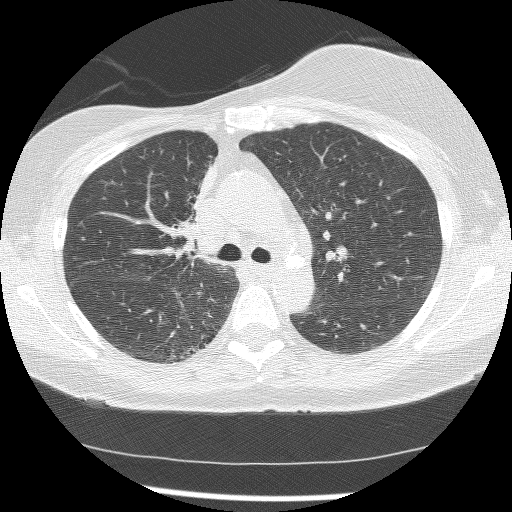
Chest CT (low-dose screening protocol), one axial image, baseline annual screen, lung window (W 1500 / L -600 HU), 2.5 mm slice thickness, slice 53 of 172 in the series. Female, age 56 years at enrolment.
Expert-annotated lung lesion, box from (x=162, y=163) to (x=218, y=263) px. The screening reader recorded 2 non-calcified nodules or masses ≥4 mm on this exam (right lower lobe, right middle lobe); which of them this box marks is not recorded. Later outcome: lung cancer diagnosed 1185 days after this screen (after the third annual screen) — adenocarcinoma, NOS, right upper lobe, stage IIIB (AJCC 6th edition), 8 mm at pathology.